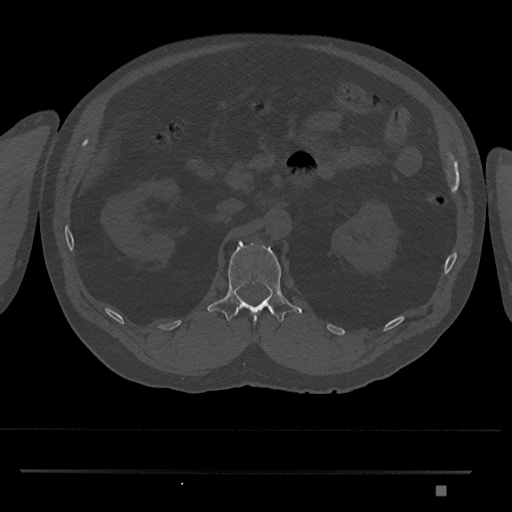
CT including the spine, one axial slice; slice 826 of 1134 in the series (ordered by position); 120 kVp; bone window (W 1800 / L 400 HU); 0.5 mm slice thickness; 512 × 512 image matrix, field of view 429 × 429 mm. Patient: male, 65 years. From the clinical record (not read from this slice): primary cancer: prostate.
Annotated regions visible in this slice (semi-automatically segmented with operator editing):
- L1 vertebra: bounding box <207,241,302,325> (left, top, right, bottom; pixels)